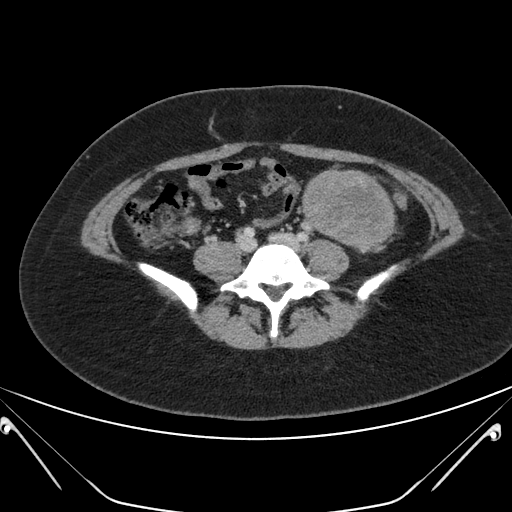
Contrast-enhanced abdominal CT, one axial slice. Slice 69 of 168 in the series (ordered by position). 120 kVp. Intravenous contrast given. Soft-tissue window (W 400 / L 40 HU). 512 × 512 image matrix, field of view 394 × 394 mm. Female patient, age 26 years. From the clinical record (not read from this slice): diagnosis: adrenocortical carcinoma; tumour side: left adrenal; tumour size at pathology: 28 cm; Ki-67 index: 20 %; stage (as recorded): 2.
Annotated regions visible in this slice (semi-automatic segmentation, software-assisted and operator-edited):
- mass: bounding box [x1, y1, x2, y2] px = [303, 170, 393, 248]